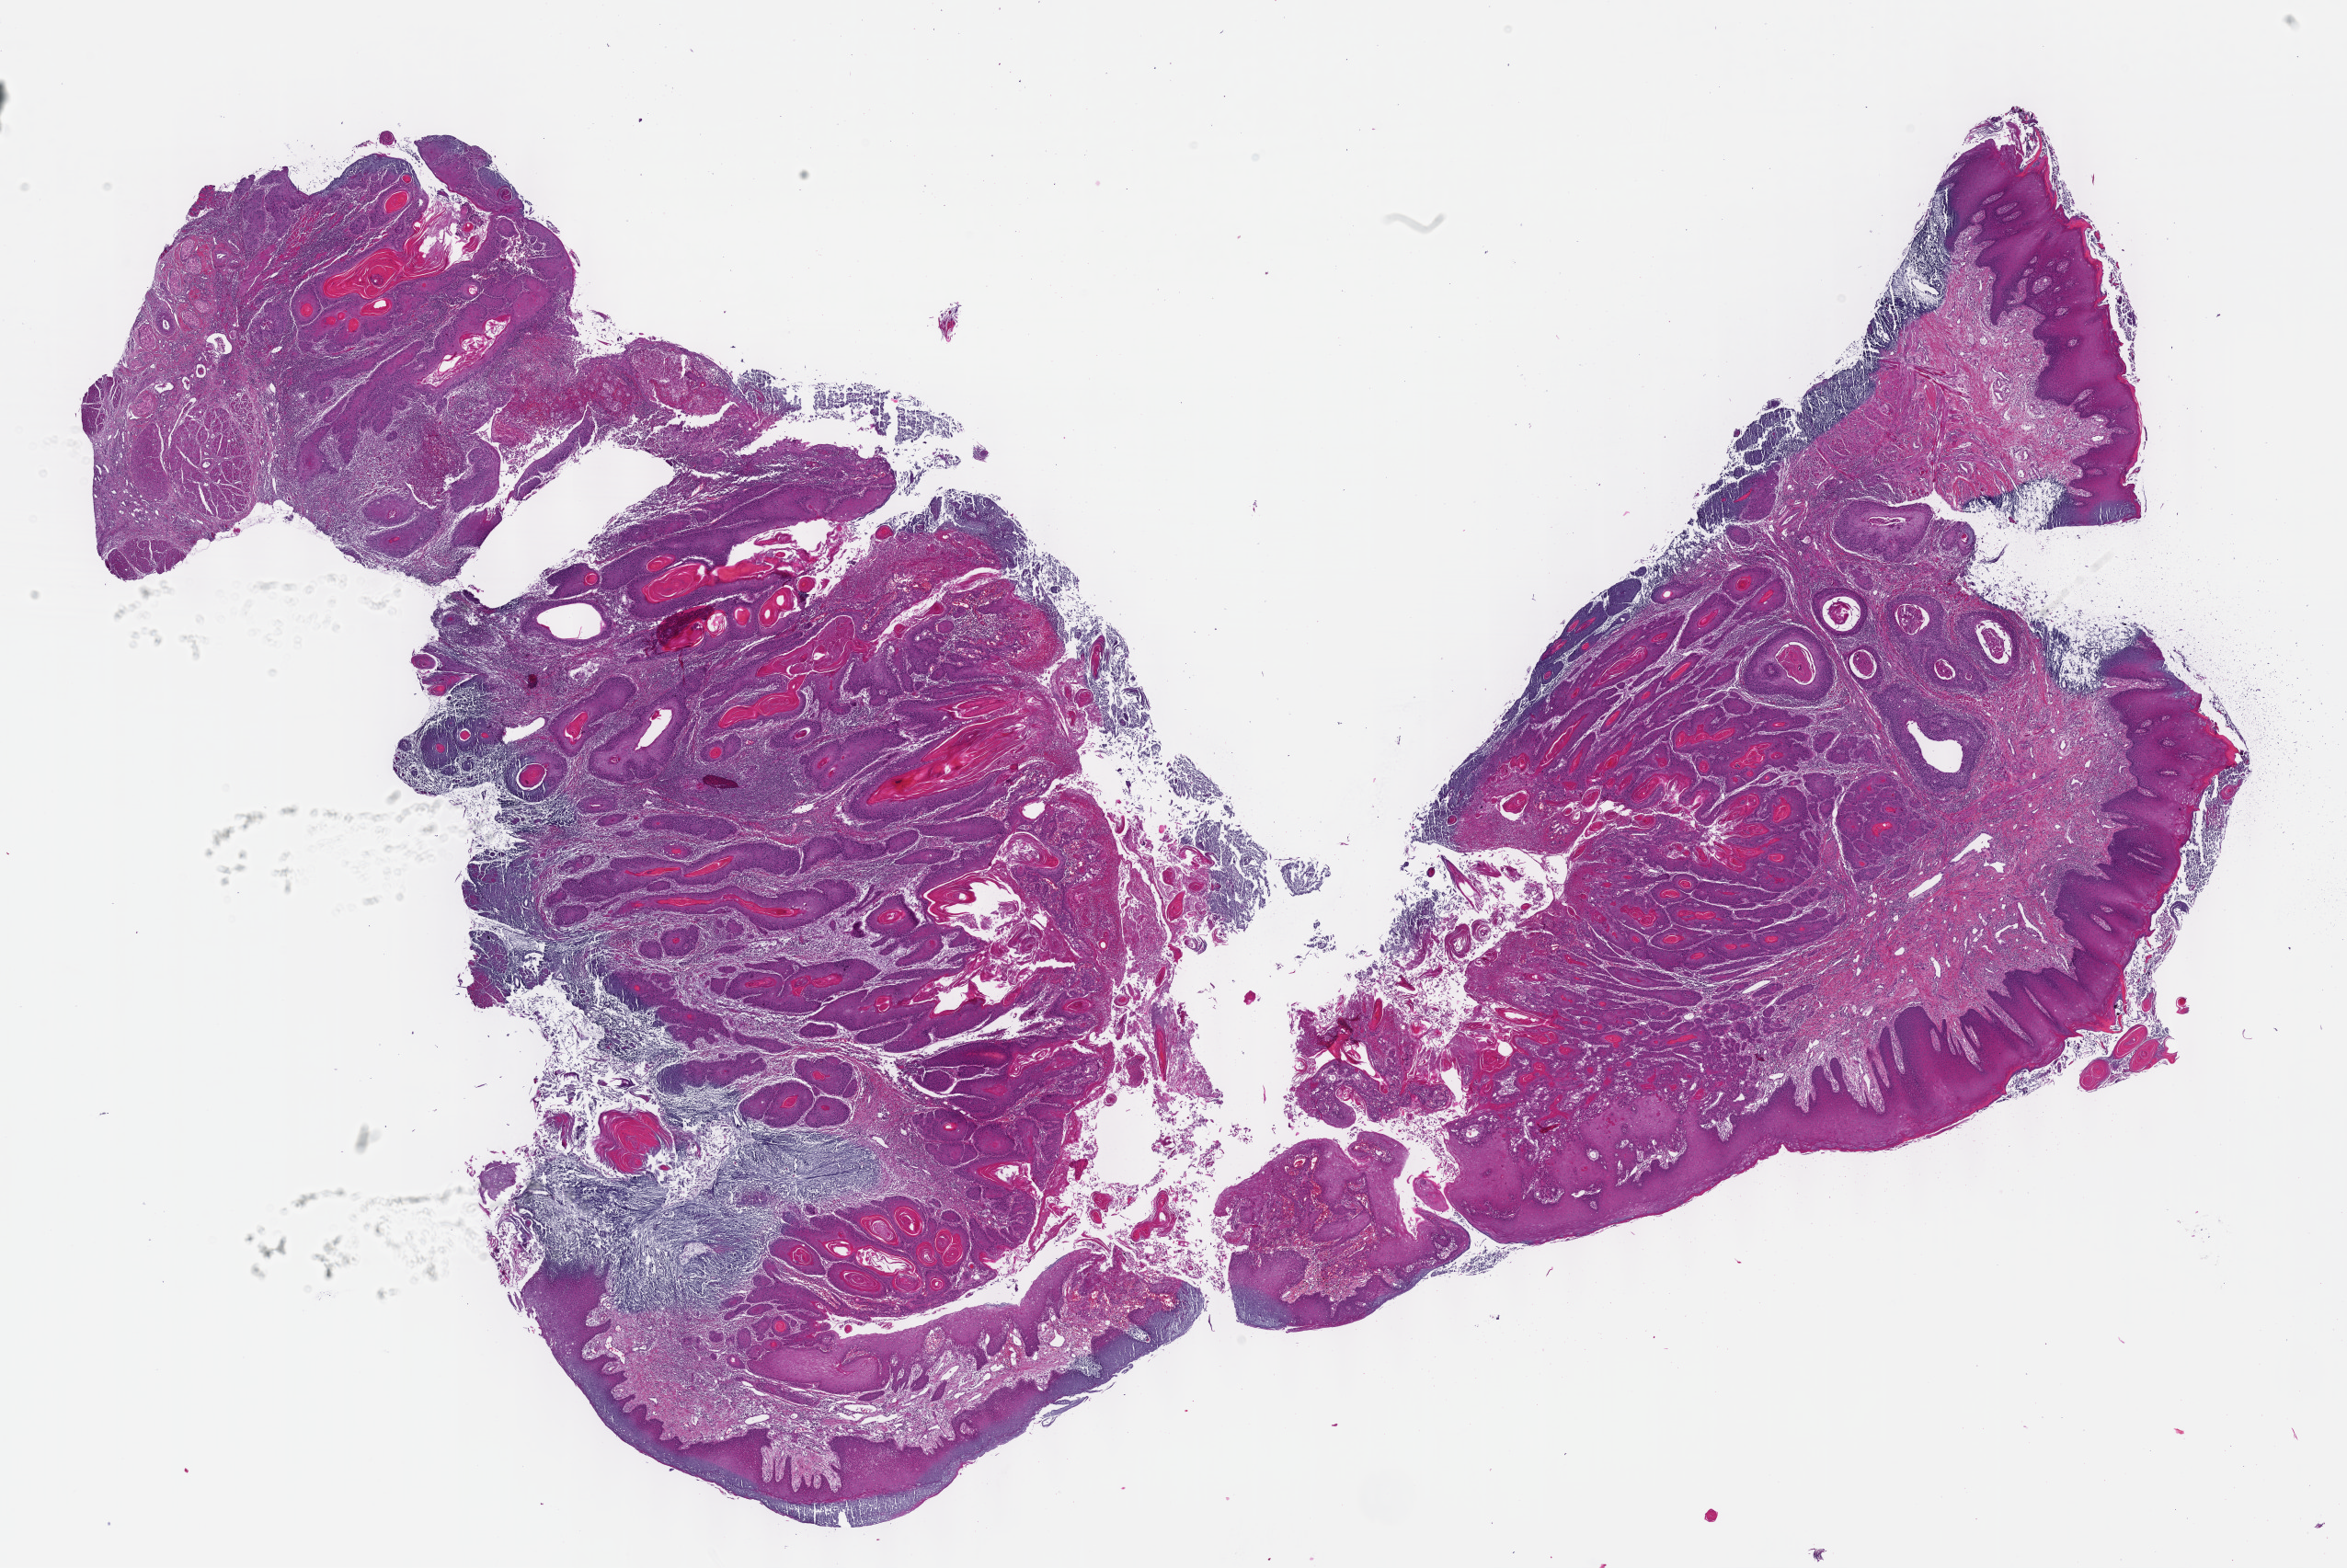
Whole-slide histology image, H&E-stained, a low-resolution overview of the entire scanned area, about 20.6 x 13.8 mm (slide scanned at 40x). Formalin-fixed paraffin-embedded (FFPE) diagnostic section. Sample: primary tumour, head and neck. Male, age 34 years at initial diagnosis.
Pathologic diagnosis: Squamous cell carcinoma, NOS (tongue, NOS).